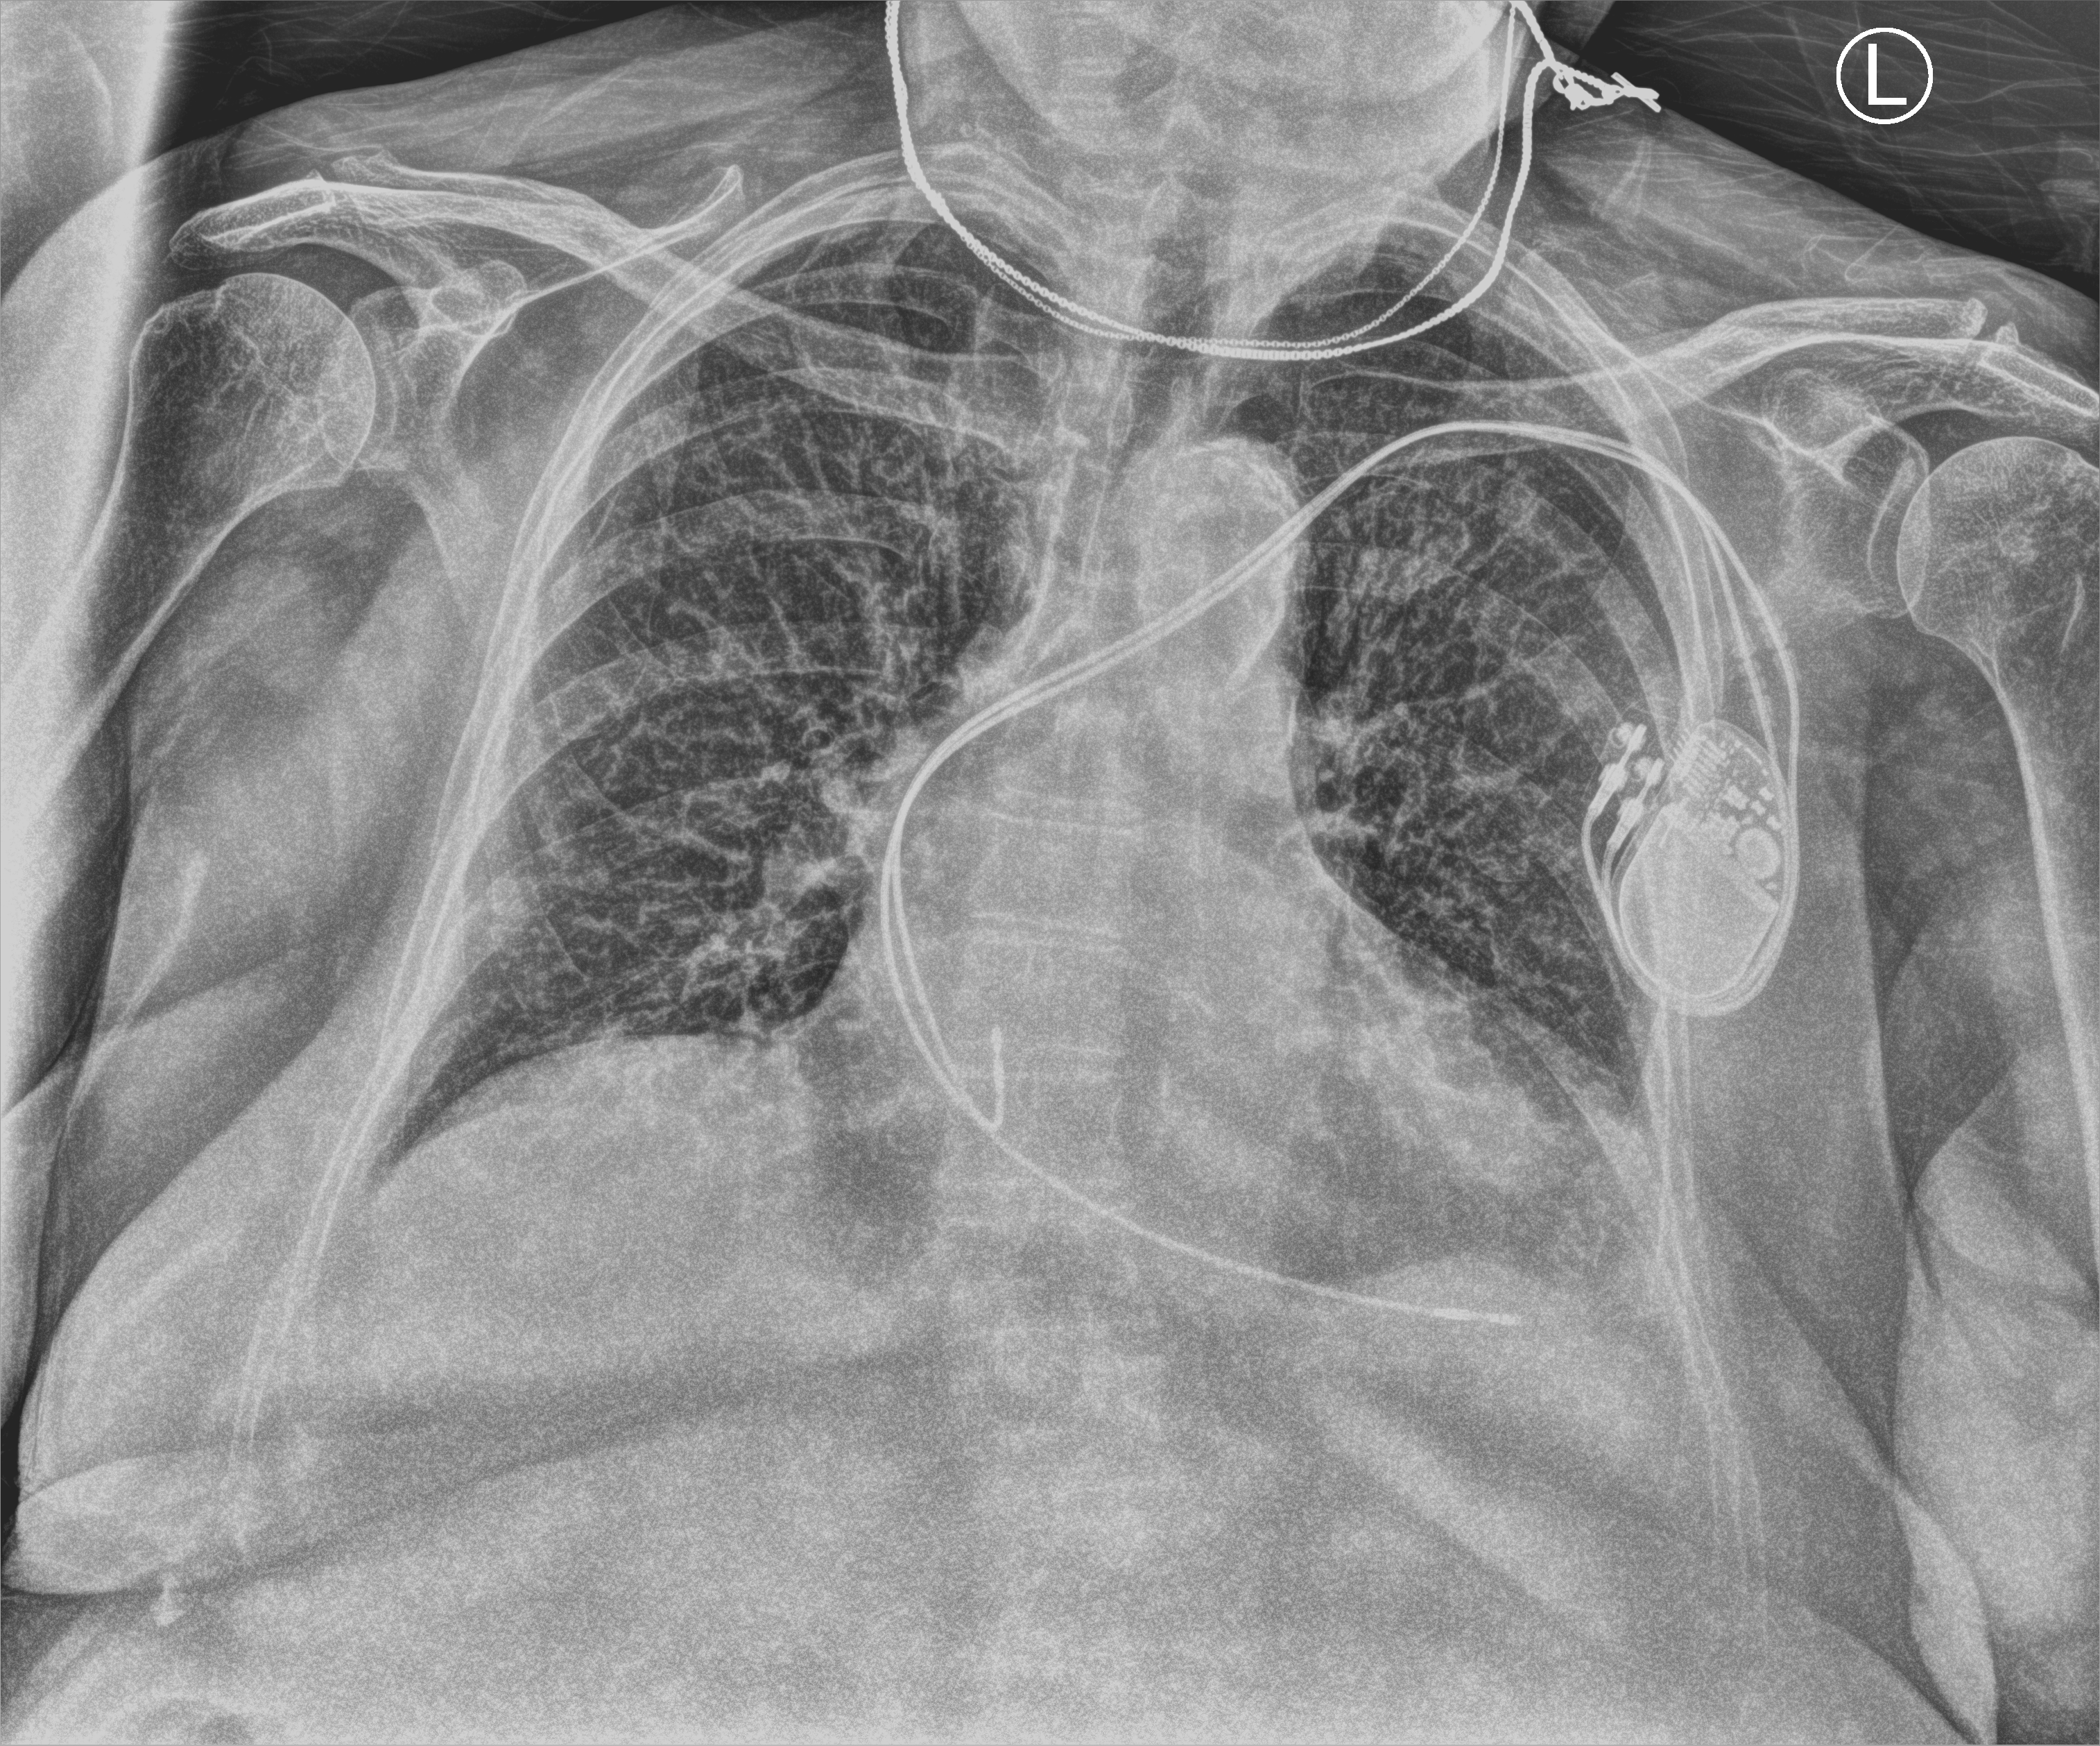
Chest X-ray (portable); anteroposterior (AP) projection. Female patient hospitalised with COVID-19, age 75–90 years.
From the hospital-stay record, not from the radiograph (when in the stay this image was taken is not recorded): admitted to intensive care during this hospital stay: no; other chronic lung disease (admission record): no.